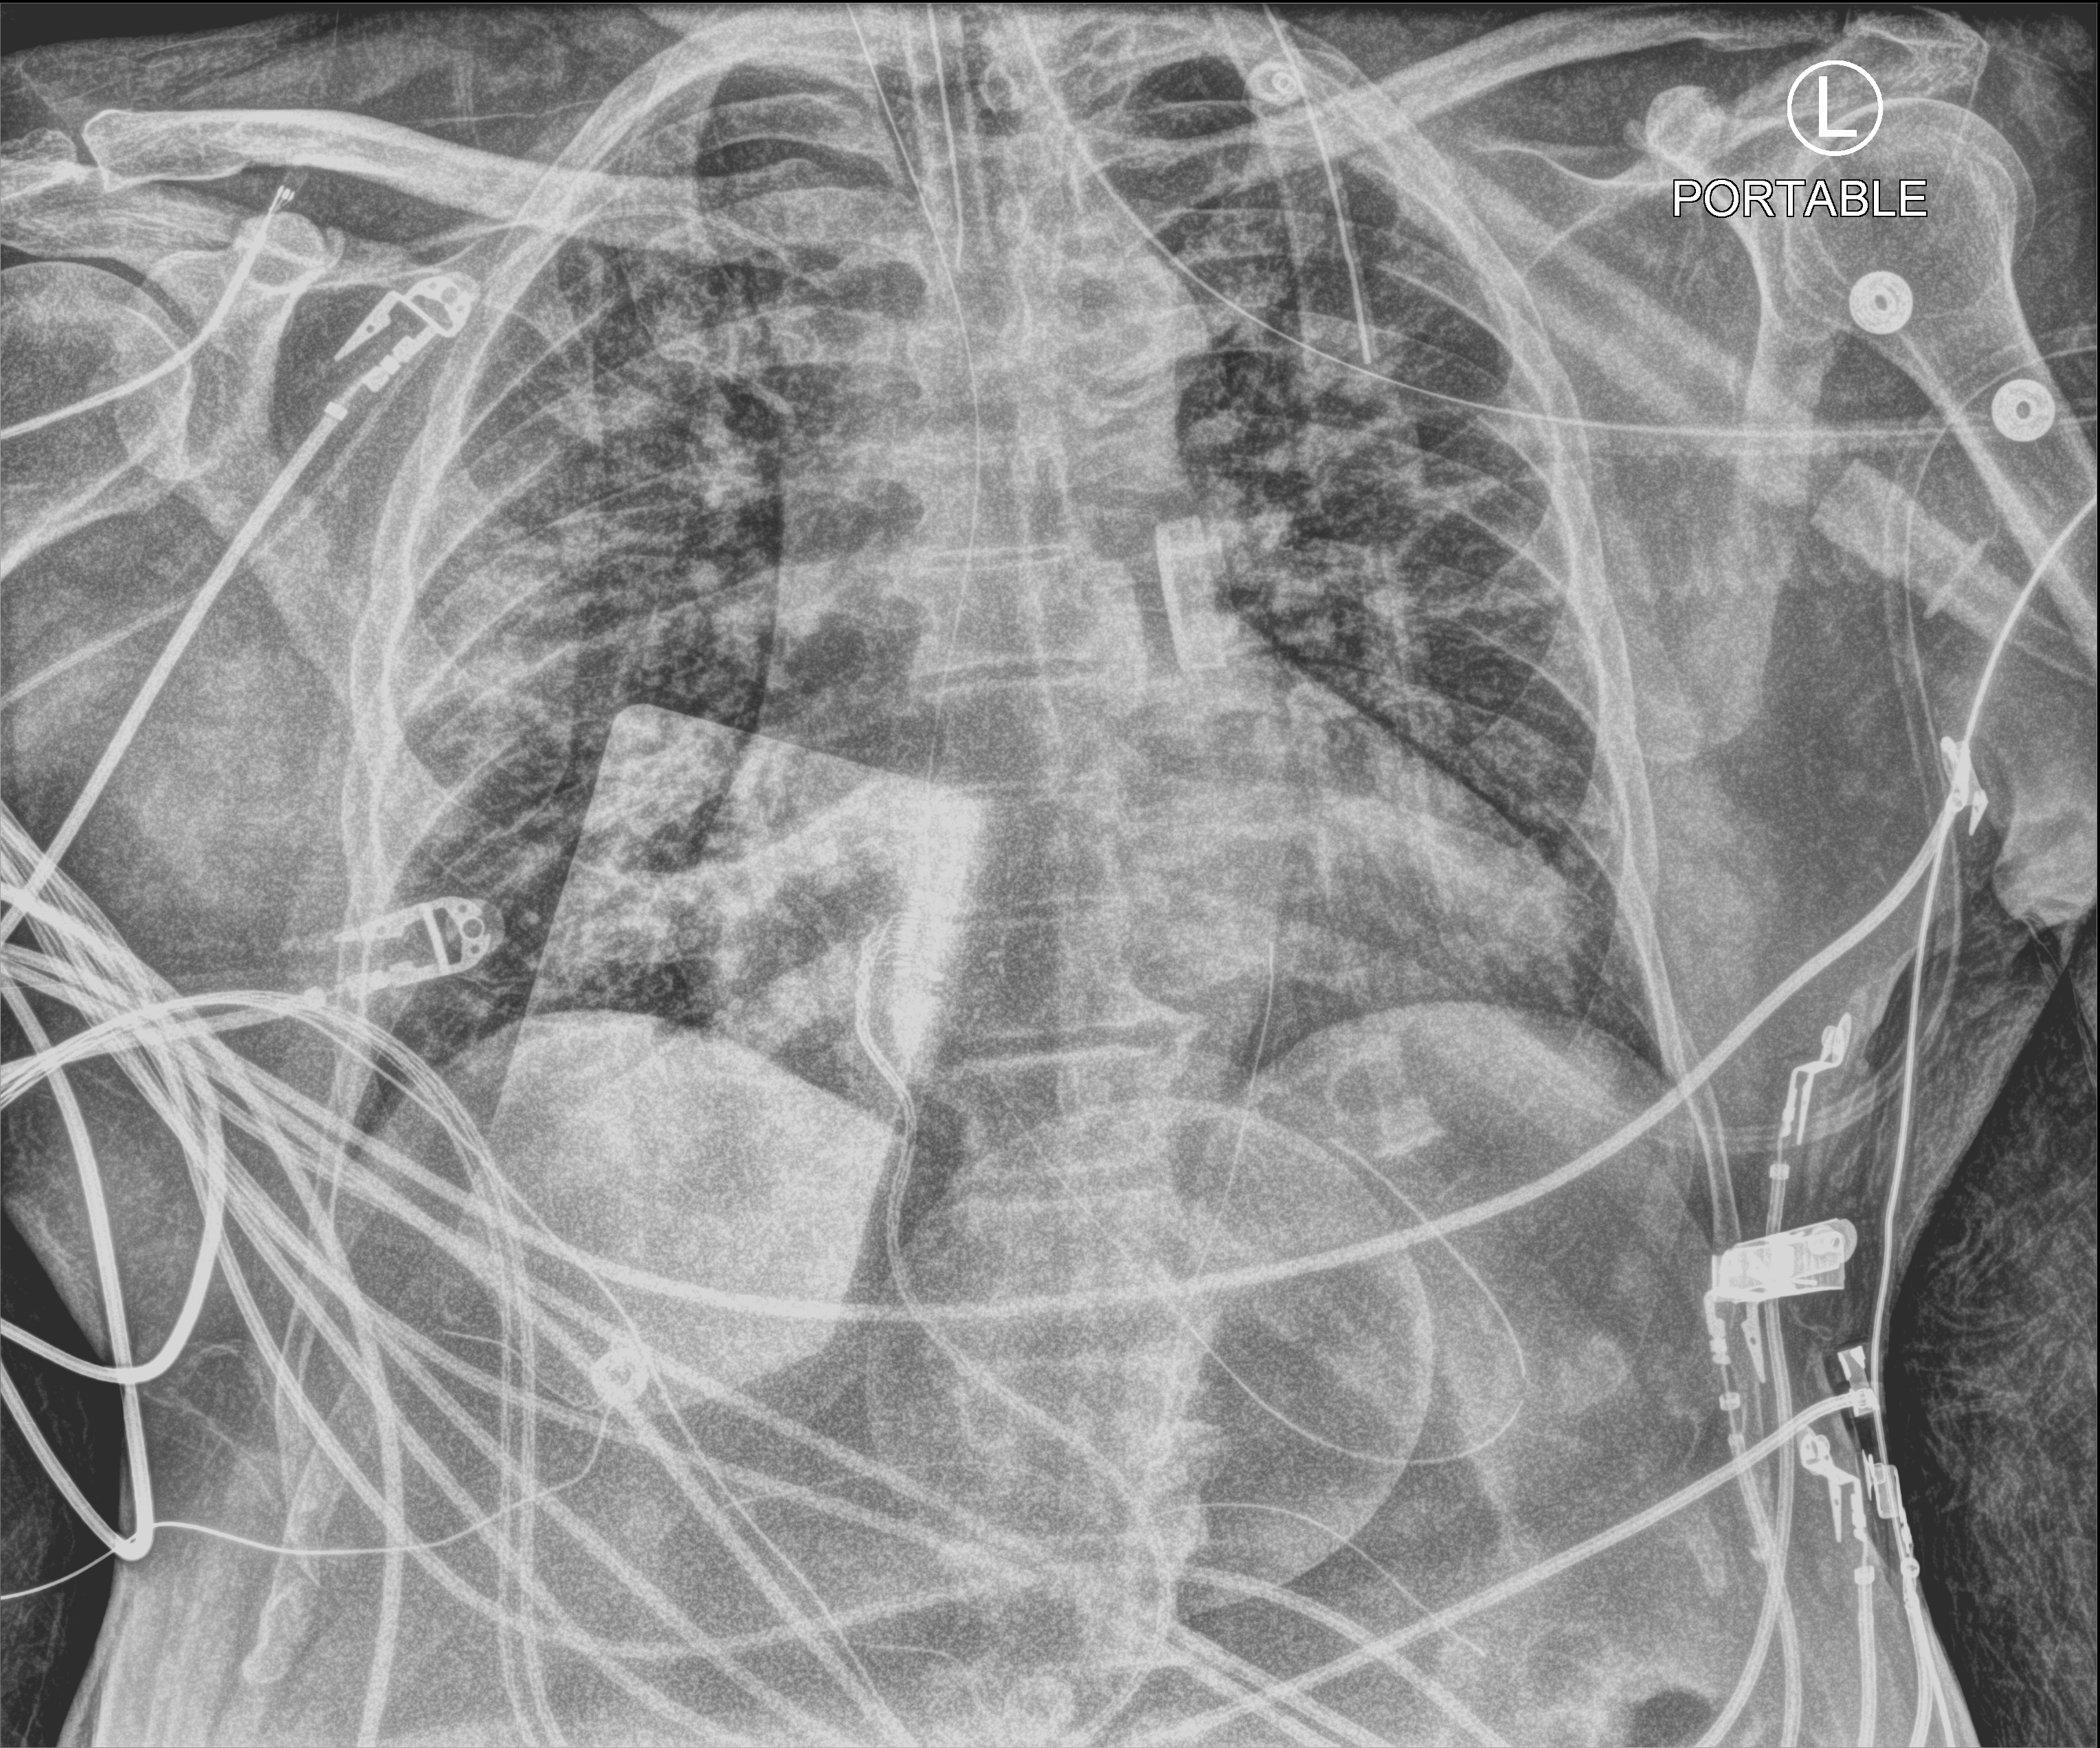
Portable chest radiograph; anteroposterior (AP) projection. Patient hospitalised with COVID-19; male, aged 60–74 years.
Admission-level facts for this patient (not findings on this image; timing relative to this image not recorded):
- hypertension (admission record): yes